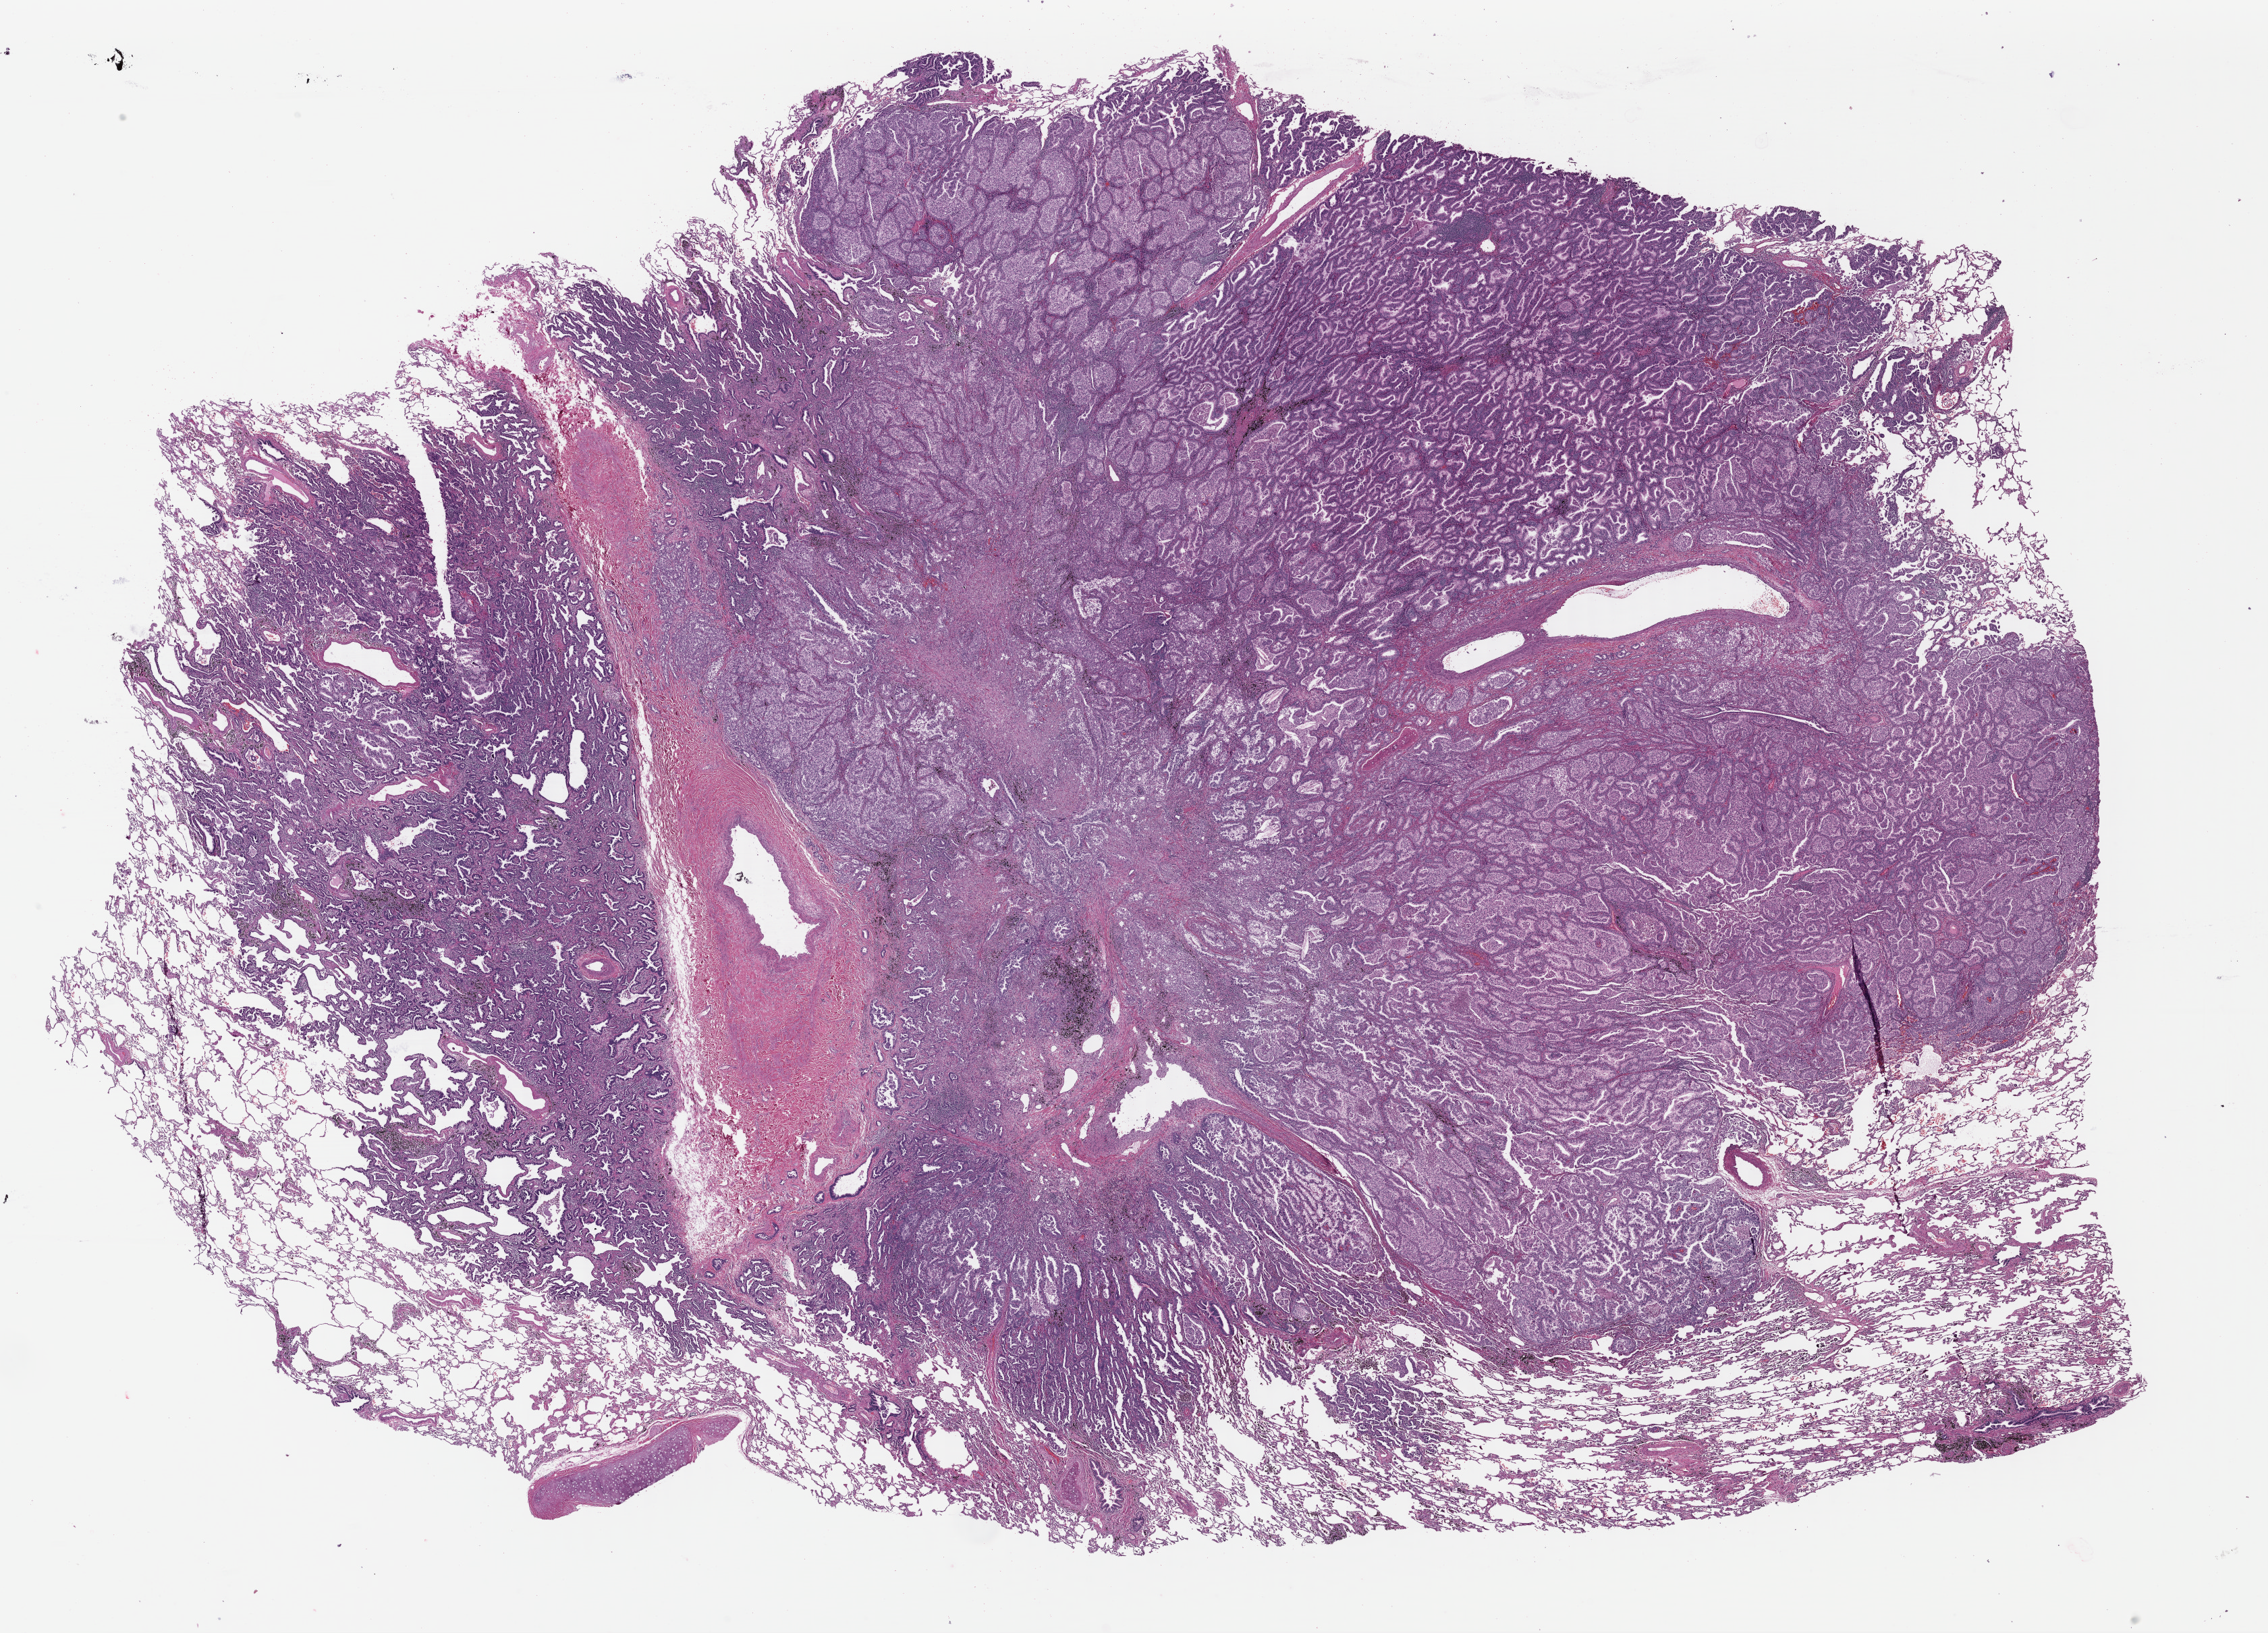
Digitized H&E tissue section (whole slide) — low-resolution overview of the scanned area, about 26.4 x 19.0 mm; formalin-fixed paraffin-embedded (FFPE) diagnostic section; primary tumour sample from the lung. Male patient; age at initial diagnosis 75 years.
Diagnosis: Adenocarcinoma with mixed subtypes (lower lobe, lung).